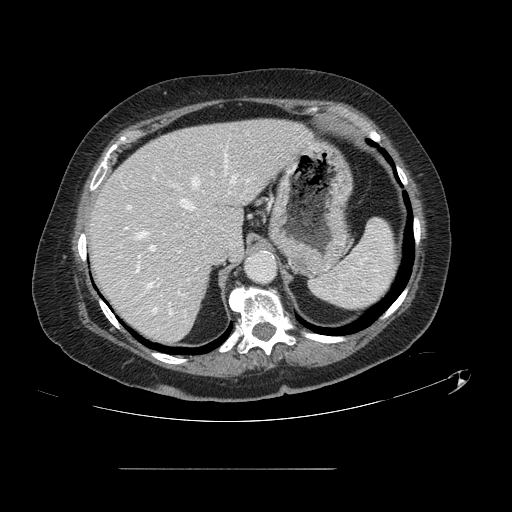
Contrast-enhanced abdominal CT, one axial slice. Position 99 of 148 along the scan axis. 120 kVp. Soft-tissue window (W 400 / L 40 HU). 512 × 512 image matrix, field of view 439 × 439 mm. Female patient, age 75 years. From the clinical record (not read from this slice): diagnosis: colorectal cancer liver metastases, imaged before liver resection.
Outlined on this slice (manually delineated by an expert):
- hepatic veins: bounding box [x1, y1, x2, y2] px = [137, 168, 250, 312]
- liver: [90, 119, 308, 343]
- planned liver remnant (the part of the liver to remain after resection): [90, 119, 309, 343]
- portal vein (with intrahepatic branches): [127, 176, 156, 272]